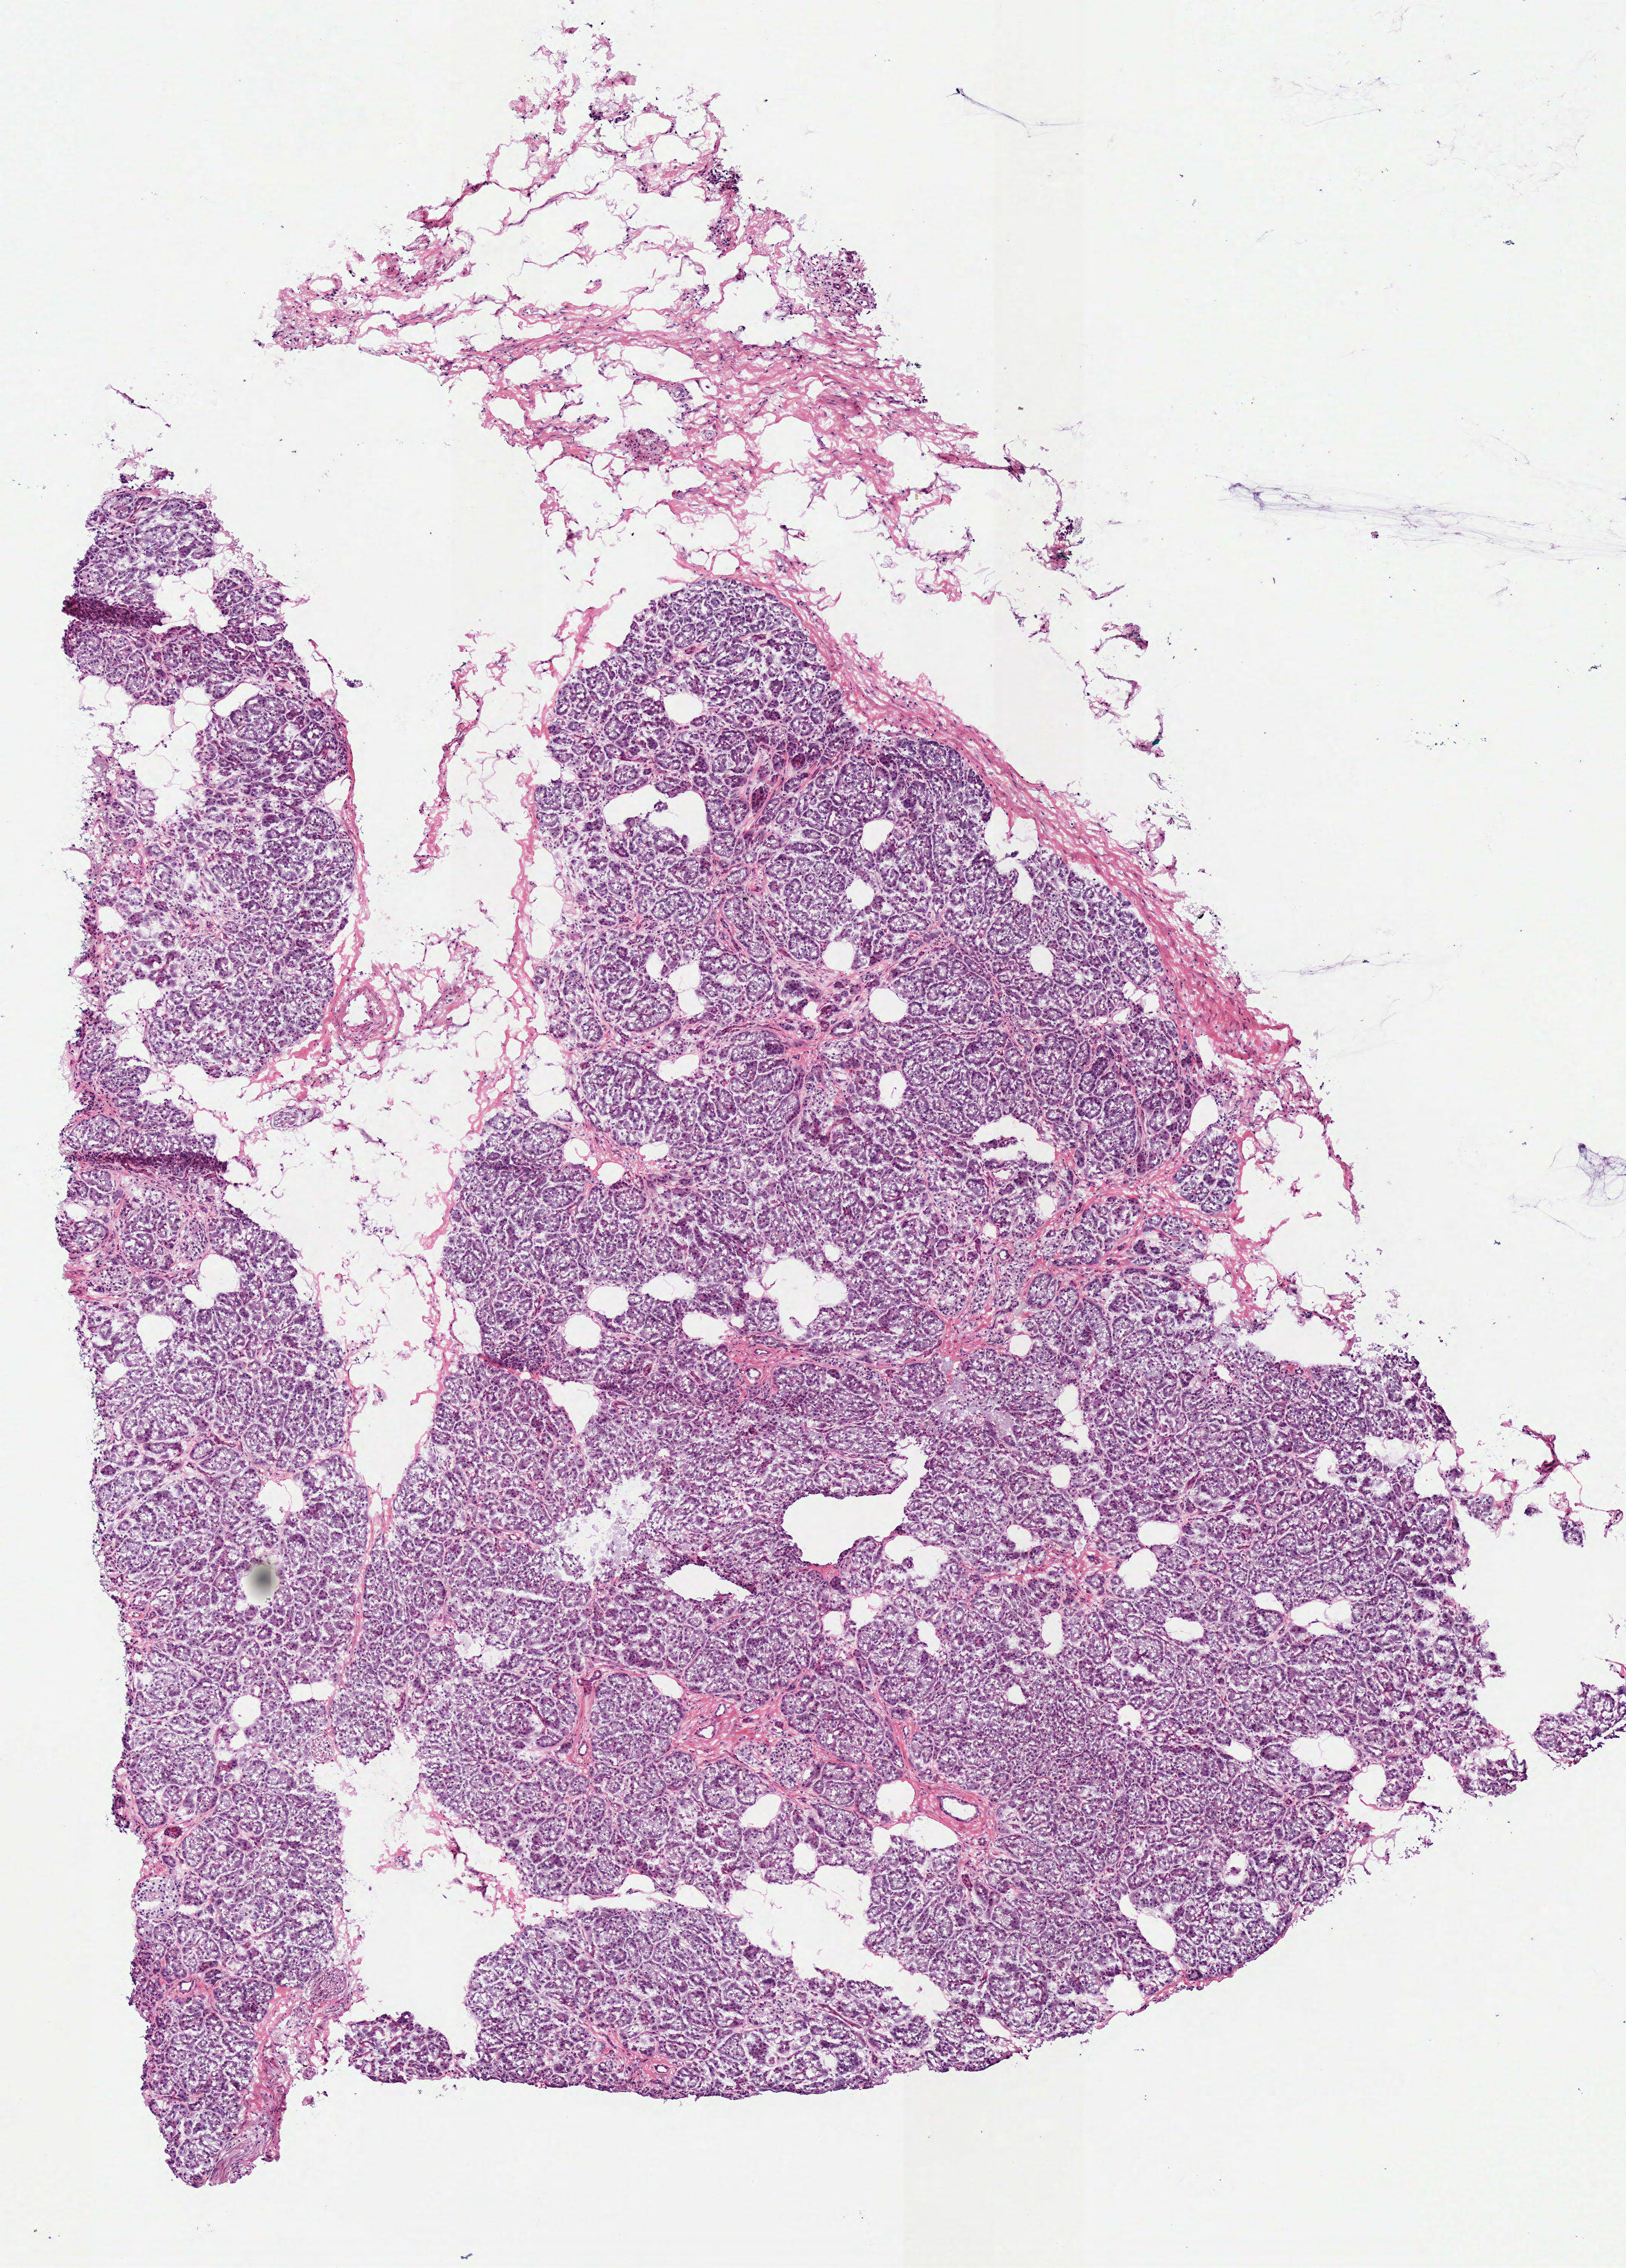
H&E-stained whole-slide image — shown as a low-resolution overview of the whole scanned area (about 4.2 x 5.9 mm). Frozen section from the top of the tissue portion. Pancreas, primary tumour sample. Male patient; age at initial diagnosis 70 years. Histologic grade: G1 (well differentiated). Slide review estimates, as recorded: tumour cells 93%, tumour nuclei 97%, normal cells 5%, stromal cells 2%, necrosis 0%.
Pathologic diagnosis: Adenocarcinoma, NOS (head of pancreas). AJCC pathologic stage: IIB (6th edition). Lymph nodes positive (case pathology): 1 of 9 examined. TNM: T3 N1 M0.